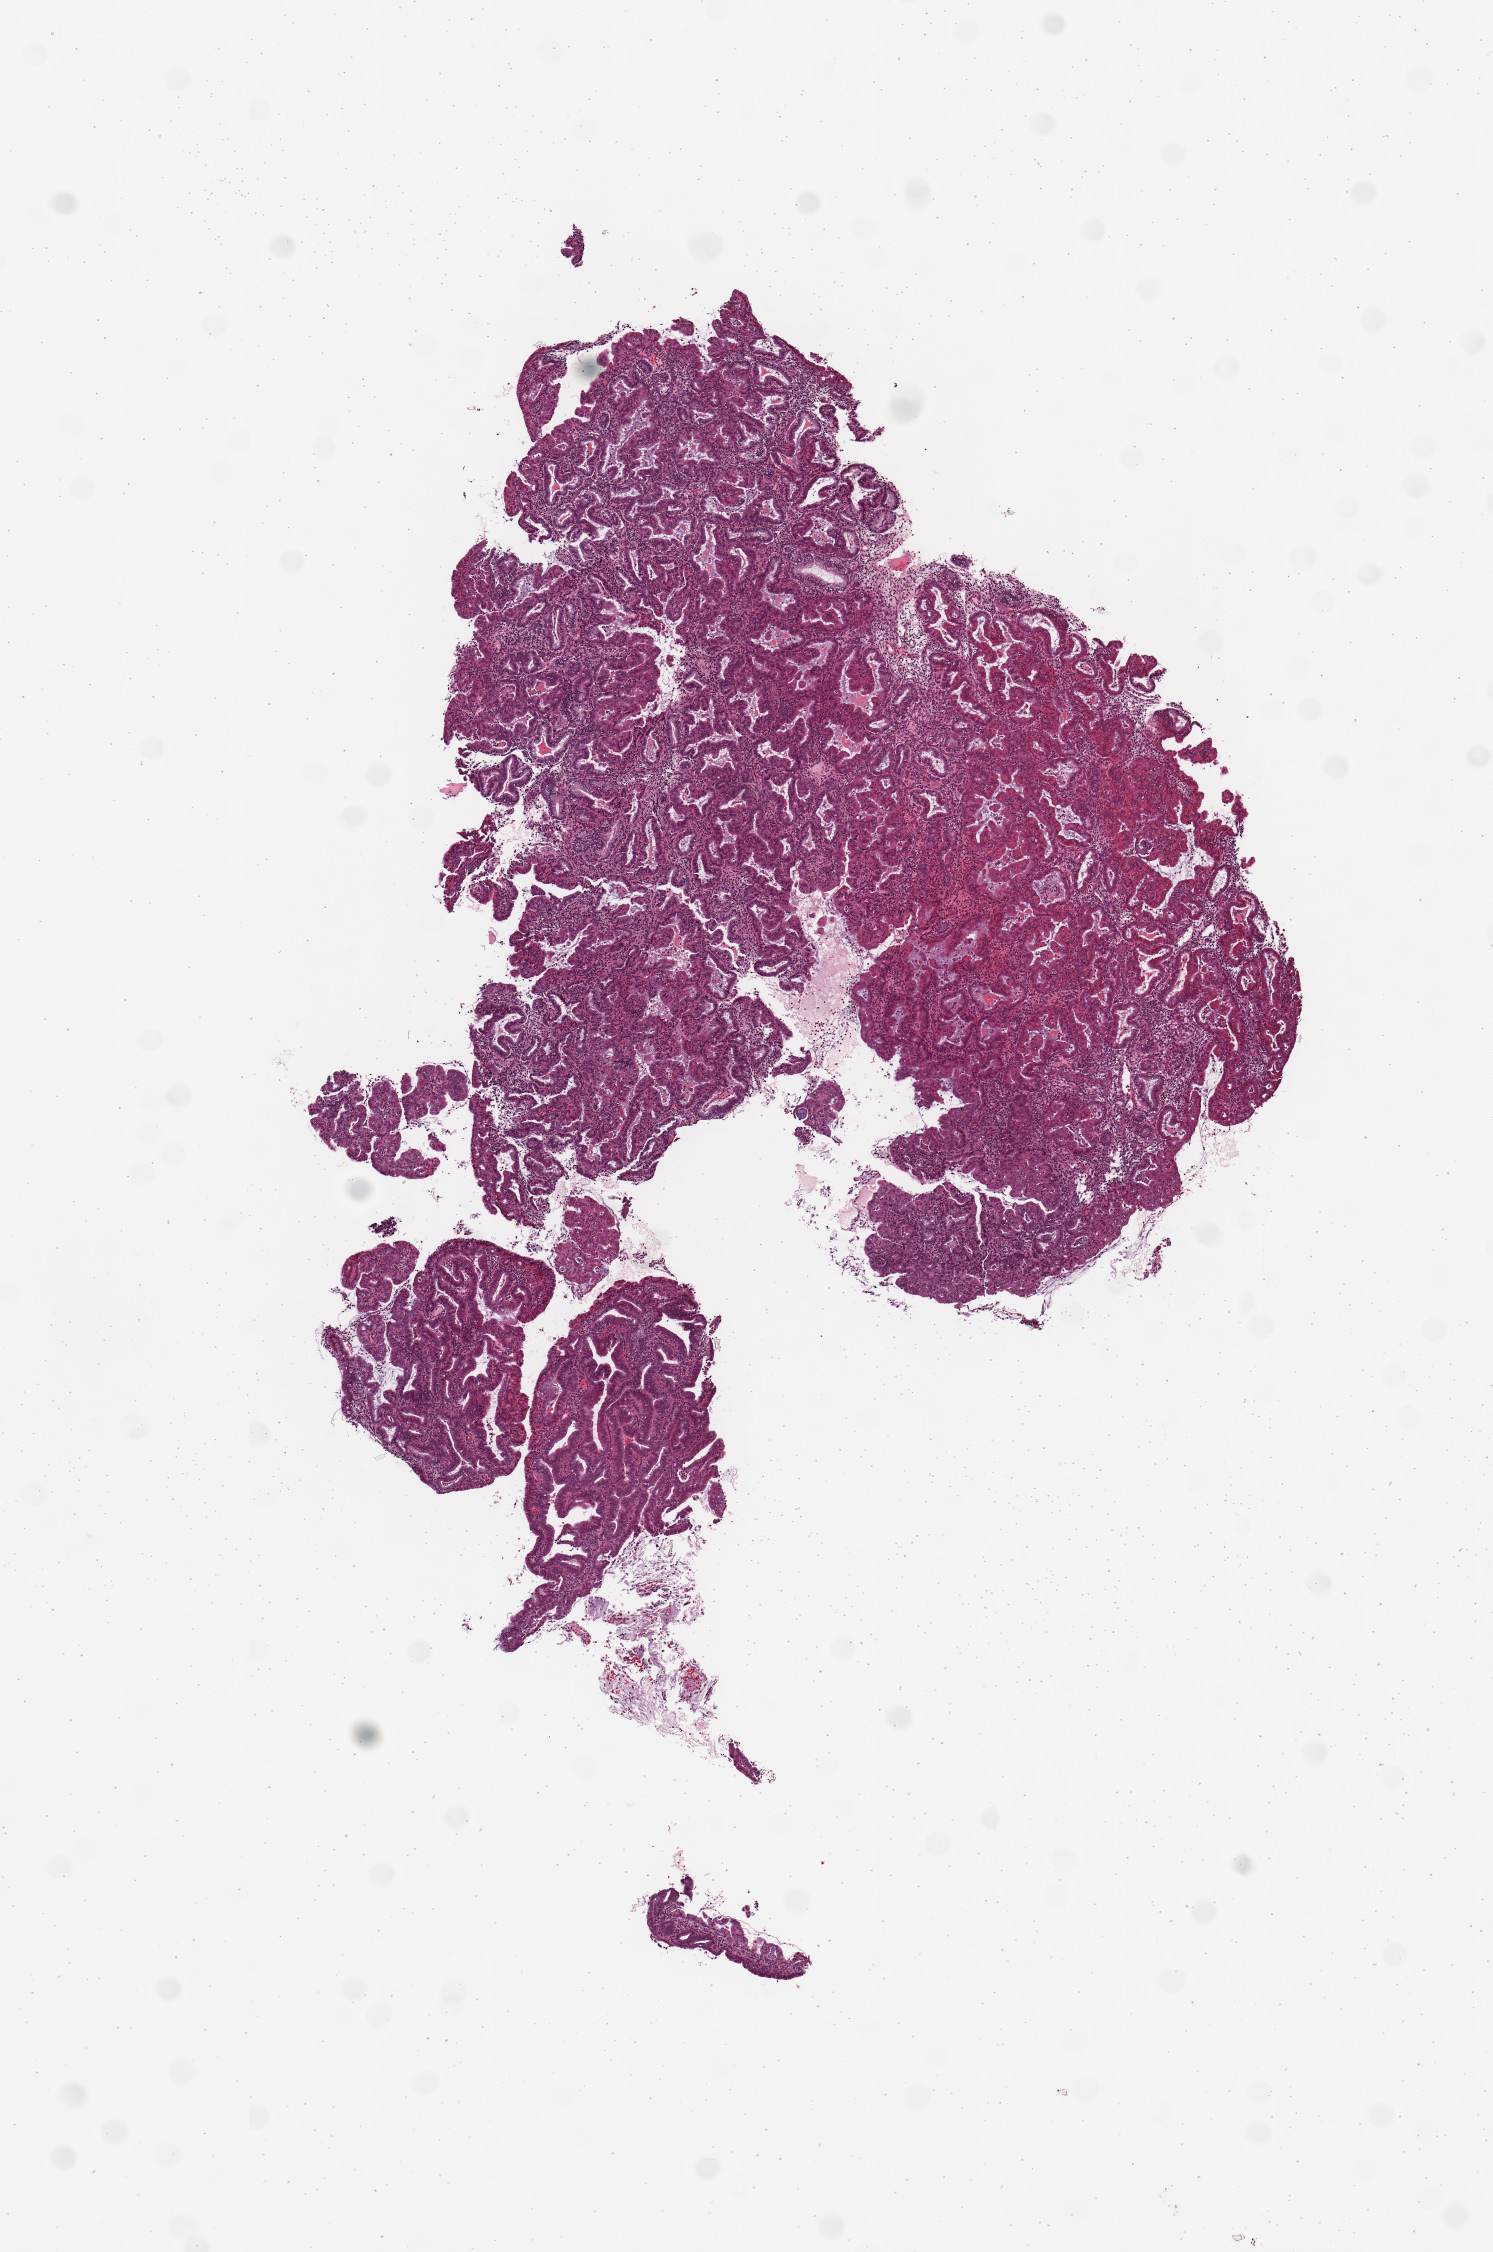
Whole-slide histology image, H&E — low-resolution overview of the scanned area, about 5.9 x 8.9 mm (from a 20x scan); uterus, tumour tissue. Female, 49 y/o.
Patient diagnosis (cohort enrolment): corpus endometrial carcinoma (uterus).